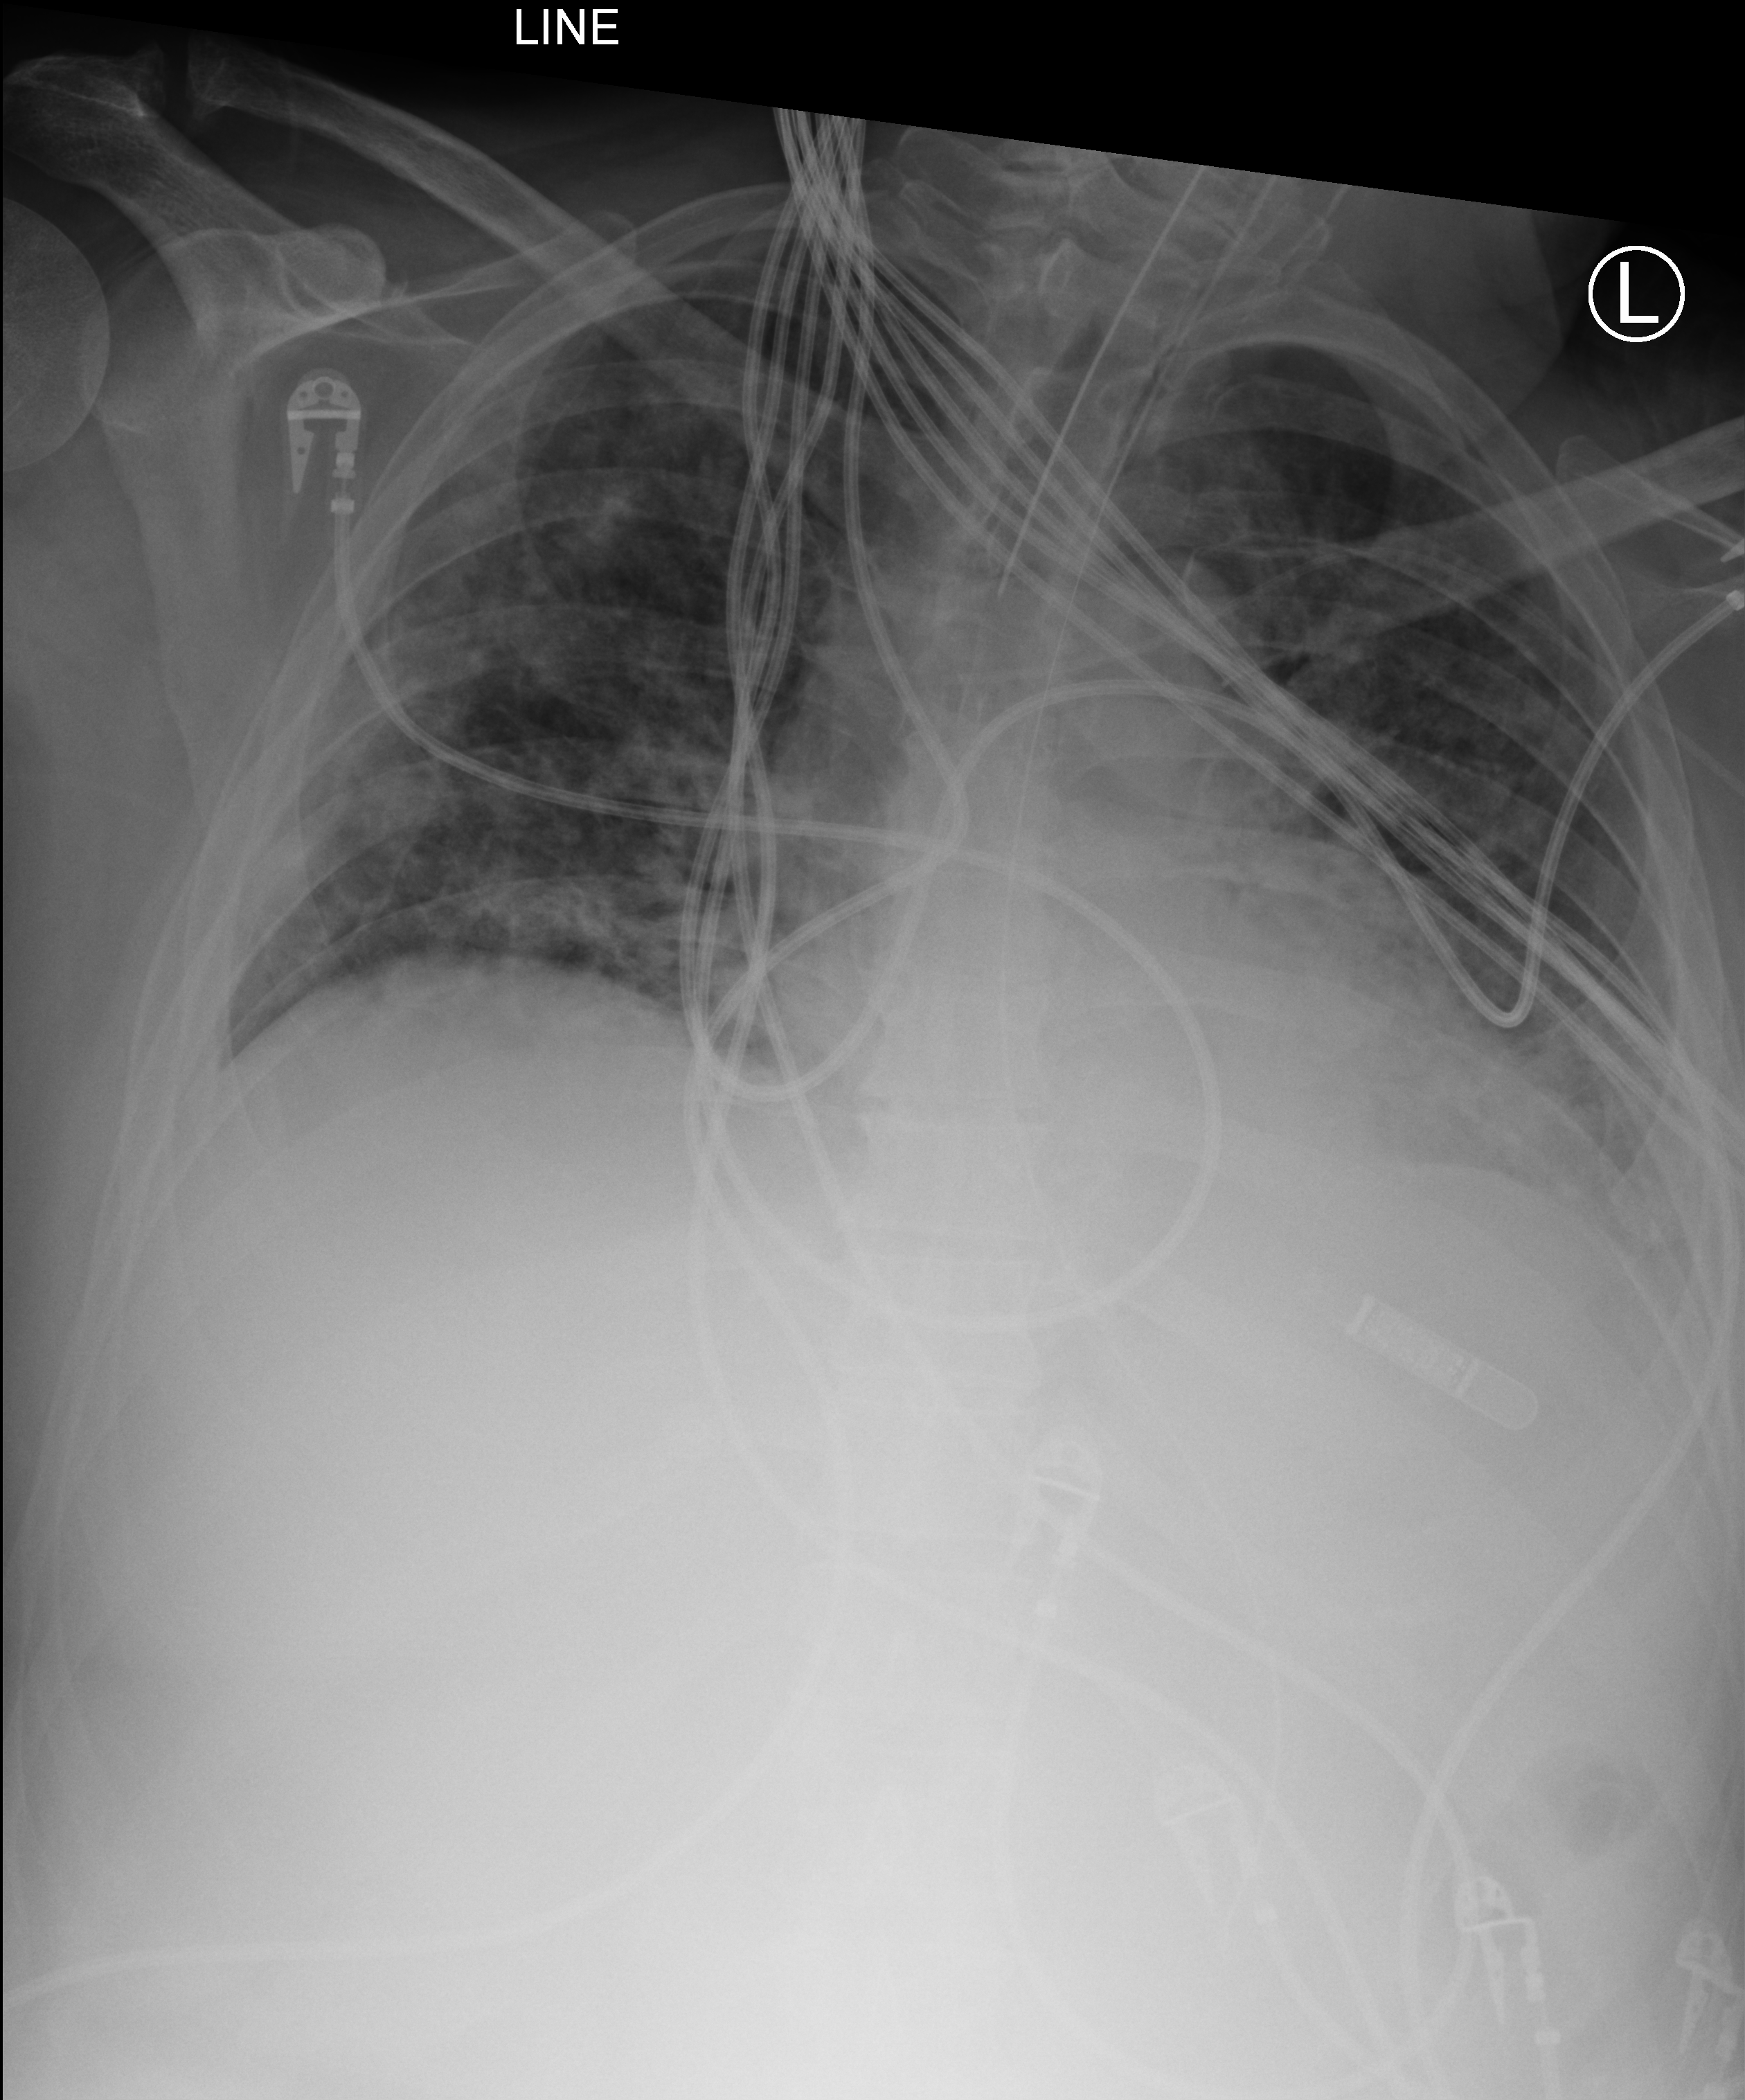
Chest X-ray (portable), anteroposterior (AP) projection. Male patient hospitalised with COVID-19, age 18–59 years.
Hospital-stay facts (about this admission, not read from this image; timing relative to this image not recorded): smoking status (admission record): former; admitted to intensive care during this hospital stay: yes.